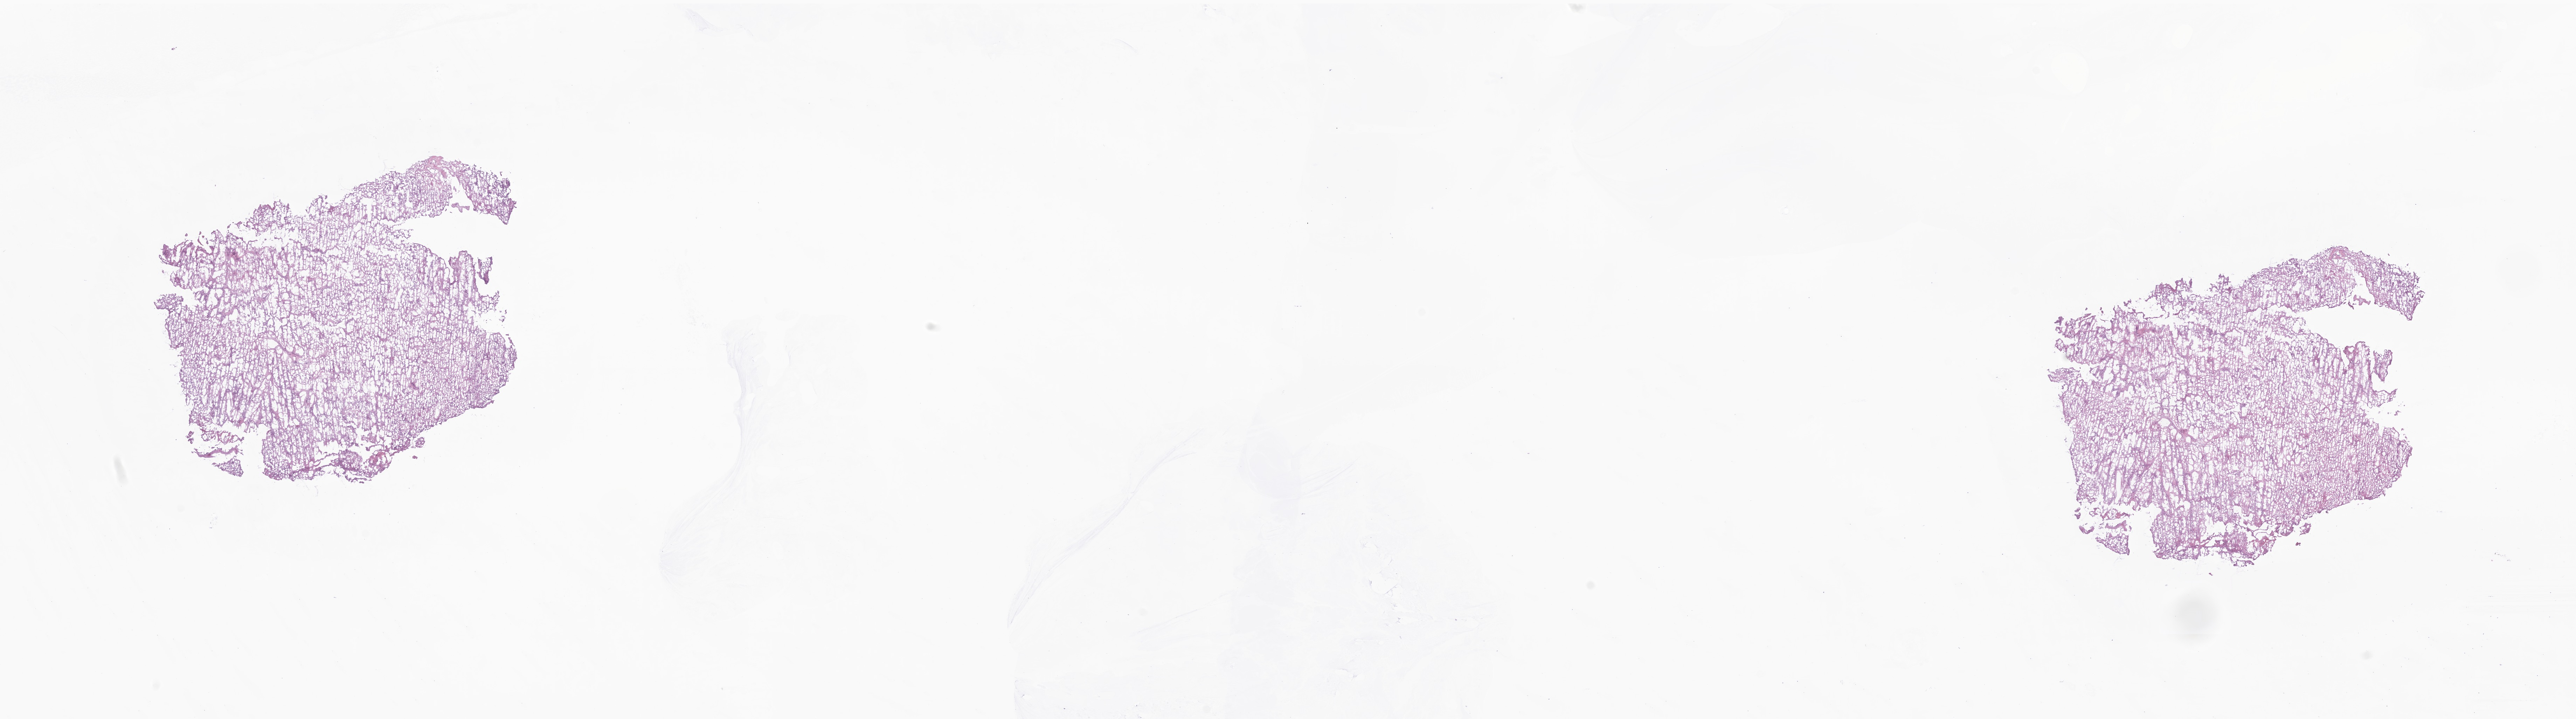
Digitized H&E-stained section of tumor tissue from the brain stem — whole scanned area (about 31.0 x 8.7 mm) shown as a low-resolution overview; frozen section. Patient male; age 44 months (3 years 8 months).
Recorded diagnosis: Neoplasm, uncertain whether benign or malignant.